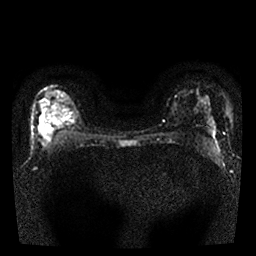
Breast MRI, one axial slice; position 17 of 25 along the scan axis; diffusion-weighted series; image 2 of 4 stored at this slice position (different b-values; order by instance number); 1.5 T; 4 mm slice thickness; 256 × 256 image matrix, field of view 300 × 300 mm. Female patient.
Outlined on this slice (outlined manually by an expert reader):
- tumour on diffusion-weighted imaging: bounding box [x1, y1, x2, y2] px = [40, 119, 51, 134]